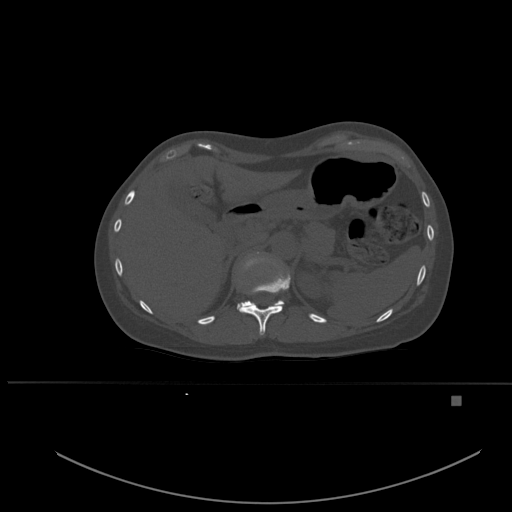
CT including the spine, one axial slice. Position 266 of 651 along the scan axis. Bone window (W 1800 / L 400 HU). 1.5 mm slice thickness. 512 × 512 image matrix, field of view 443 × 443 mm. Patient: female, 49 years. Case-level facts recorded for this patient, not image findings: primary cancer: breast; vertebrae with lytic lesions (as recorded): L3, T12, L4.
Structures marked on this image (semi-automatic segmentation, software-assisted and operator-edited):
- T11 vertebra: bounding box <238,272,291,335> (left, top, right, bottom; pixels)
- T12 vertebra: <237,252,284,309>